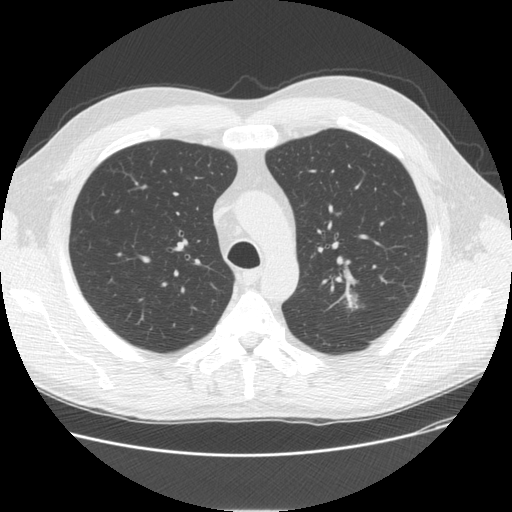
Low-dose screening chest CT, one axial slice. Lung window (W 1500 / L -600 HU). 2.5 mm slice thickness. 512 × 512 image matrix, field of view 370 × 370 mm.
Annotated regions visible in this slice (outlined manually by an expert reader):
- lesion 1 (tumor, upper lobe of left lung): box from (x=340, y=291) to (x=358, y=308) px